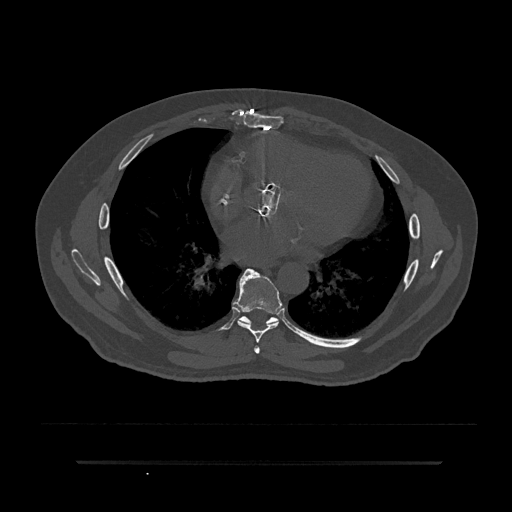
CT including the spine, one axial slice. Position 462 of 797 along the scan axis. Reconstruction kernel Br40s/3. Bone window (W 1800 / L 400 HU). 0.5 mm slice thickness. 512 × 512 image matrix, field of view 464 × 464 mm. Male patient, age 59 years. From the clinical record (not read from this slice): primary cancer: bile ducts.
Structures marked on this image (semi-automatic segmentation, software-assisted and operator-edited):
- T6 vertebra: box from (x=254, y=346) to (x=260, y=354) px
- T7 vertebra: (x=233, y=268)–(x=282, y=343)
- T8 vertebra: (x=222, y=309)–(x=297, y=334)